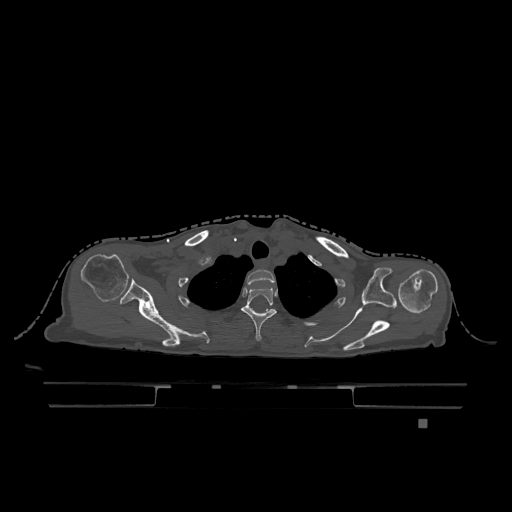
CT including the spine, one axial slice; bone window (W 1800 / L 400 HU); 512 × 512 image matrix. Patient: female, 74 years. Case-level facts recorded for this patient, not image findings: primary cancer: lung; vertebrae with lytic lesions (as recorded): T1, T4, T5, T6, L4, L5.
Structures marked on this image (semi-automatically segmented with operator editing):
- T1 vertebra: bounding box (x1, y1, x2, y2) in pixels: (247, 269, 275, 285)
- T2 vertebra: (241, 287, 277, 341)